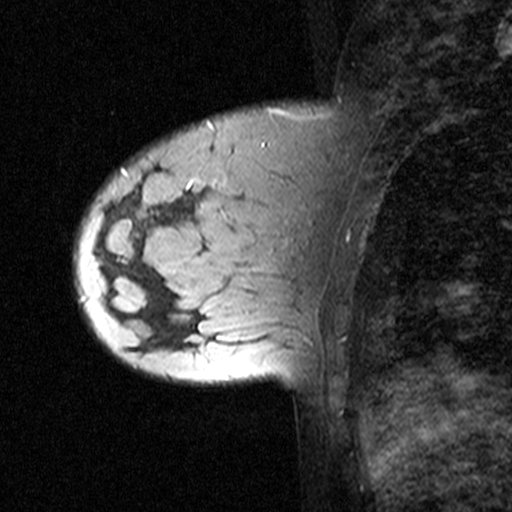
Breast MRI (dynamic contrast-enhanced), one sagittal slice. Slice 12 of 44 in the series (ordered by position). Dynamic contrast-enhanced study with each time point stored as its own series, time point 2 of 3 at this slice position (early post-contrast, ordered by acquisition time). 1.5 T. TE 4.5 ms, TR 11 ms. 3 mm slice thickness. 512 × 512 image matrix, field of view 200 × 200 mm. Female patient, age 27 years. From the clinical record (not read from this slice): setting: breast cancer imaged before/during neoadjuvant chemotherapy; receptor status: HR-positive, HER2-negative.
Annotated regions visible in this slice (semi-automatically segmented with operator editing):
- analysis volume of interest (the breast-tissue region the enhancement analysis was run in; not a lesion): bounding box [x1, y1, x2, y2] px = [74, 162, 163, 271]
- tumour enhancement mask (voxels above the 90 % enhancement threshold inside the analysis volume of interest): [120, 168, 127, 175]